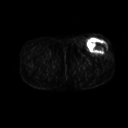
FDG PET of an extremity soft-tissue mass (from a PET/CT study), one axial slice; slice 238 of 267 in the series (ordered by position); 3.27 mm slice thickness; 128 × 128 image matrix, field of view 500 × 500 mm. Patient: male, 64 years. Case-level facts recorded for this patient, not image findings: histological type: extraskeletal osteosarcoma; grade: high; site of the primary tumour: thigh.
Annotated regions visible in this slice (expert contour drawn on MRI and transferred to this co-registered scan by the dataset authors):
- gross tumour volume (mass): bounding box [x1, y1, x2, y2] px = [88, 39, 108, 53]